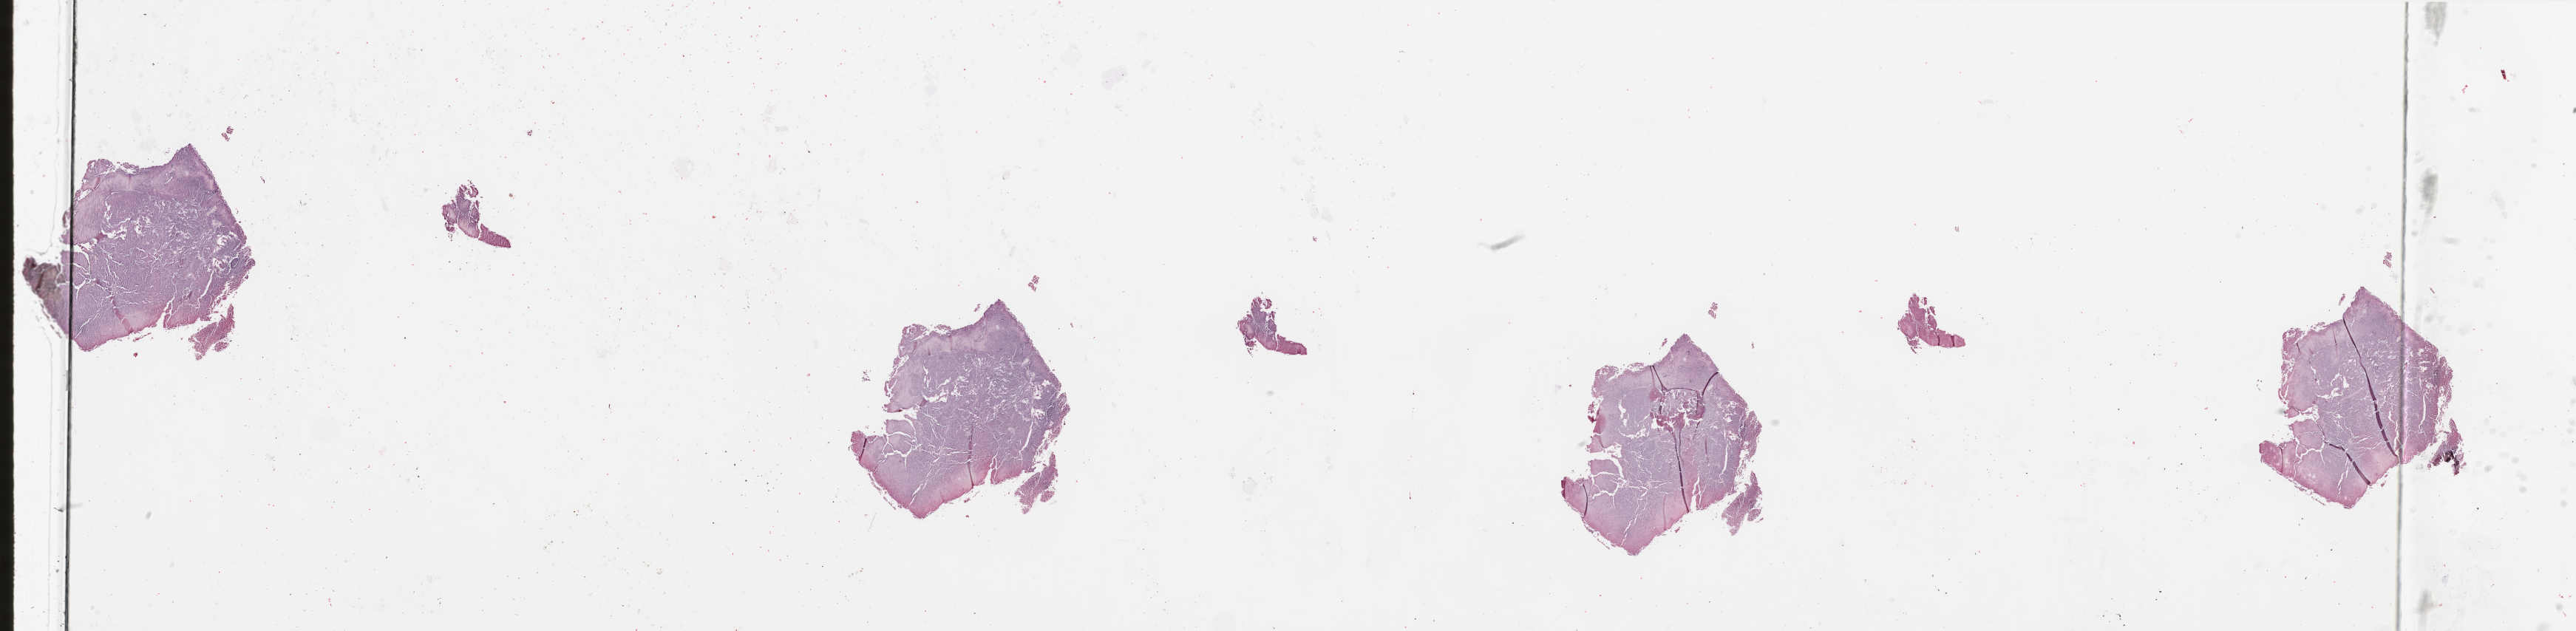
Digitized H&E tissue section (whole slide) — a low-resolution overview of the entire scanned area, about 55.1 x 13.5 mm (slide scanned at 20x). Tumour tissue sample, sampled site: lymph node. Male, 56 y/o. Pathologist review of this section (percent, as recorded): tumour nuclei 100%, necrosis 10%.
- this section: metastatic tumour tissue
- patient diagnosis: Malignant melanoma, NOS